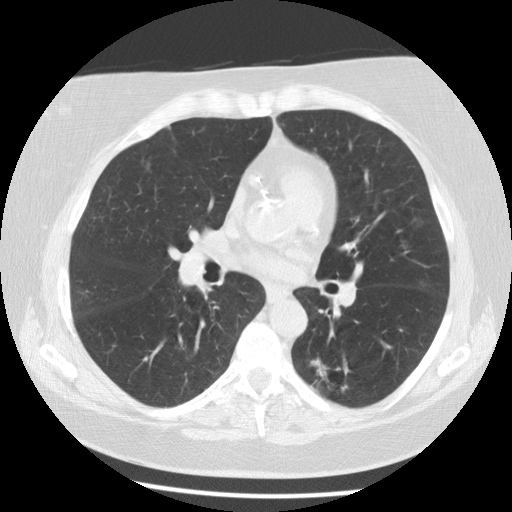
Low-dose screening chest CT, axial slice, third screening round (two years after baseline), lung window (W 1500 / L -600 HU), 2.5 mm slice thickness, standard (soft-tissue) reconstruction kernel (STANDARD), 120 kVp, 512 × 512 image matrix. Female, age 59 years at enrolment. Current smoker at enrolment.
Expert-annotated lung lesion, bounding box [x1, y1, x2, y2] px = [299, 349, 360, 407]. The screening reader recorded 6 non-calcified nodules or masses ≥4 mm on this exam; which of them this box marks is not recorded. Official screen result: positive, other. Participant outcome: lung cancer diagnosed 56 days after this screen — adenocarcinoma, NOS, left lower lobe, poorly differentiated (G3), stage IA (AJCC 6th edition), 15 mm at pathology.